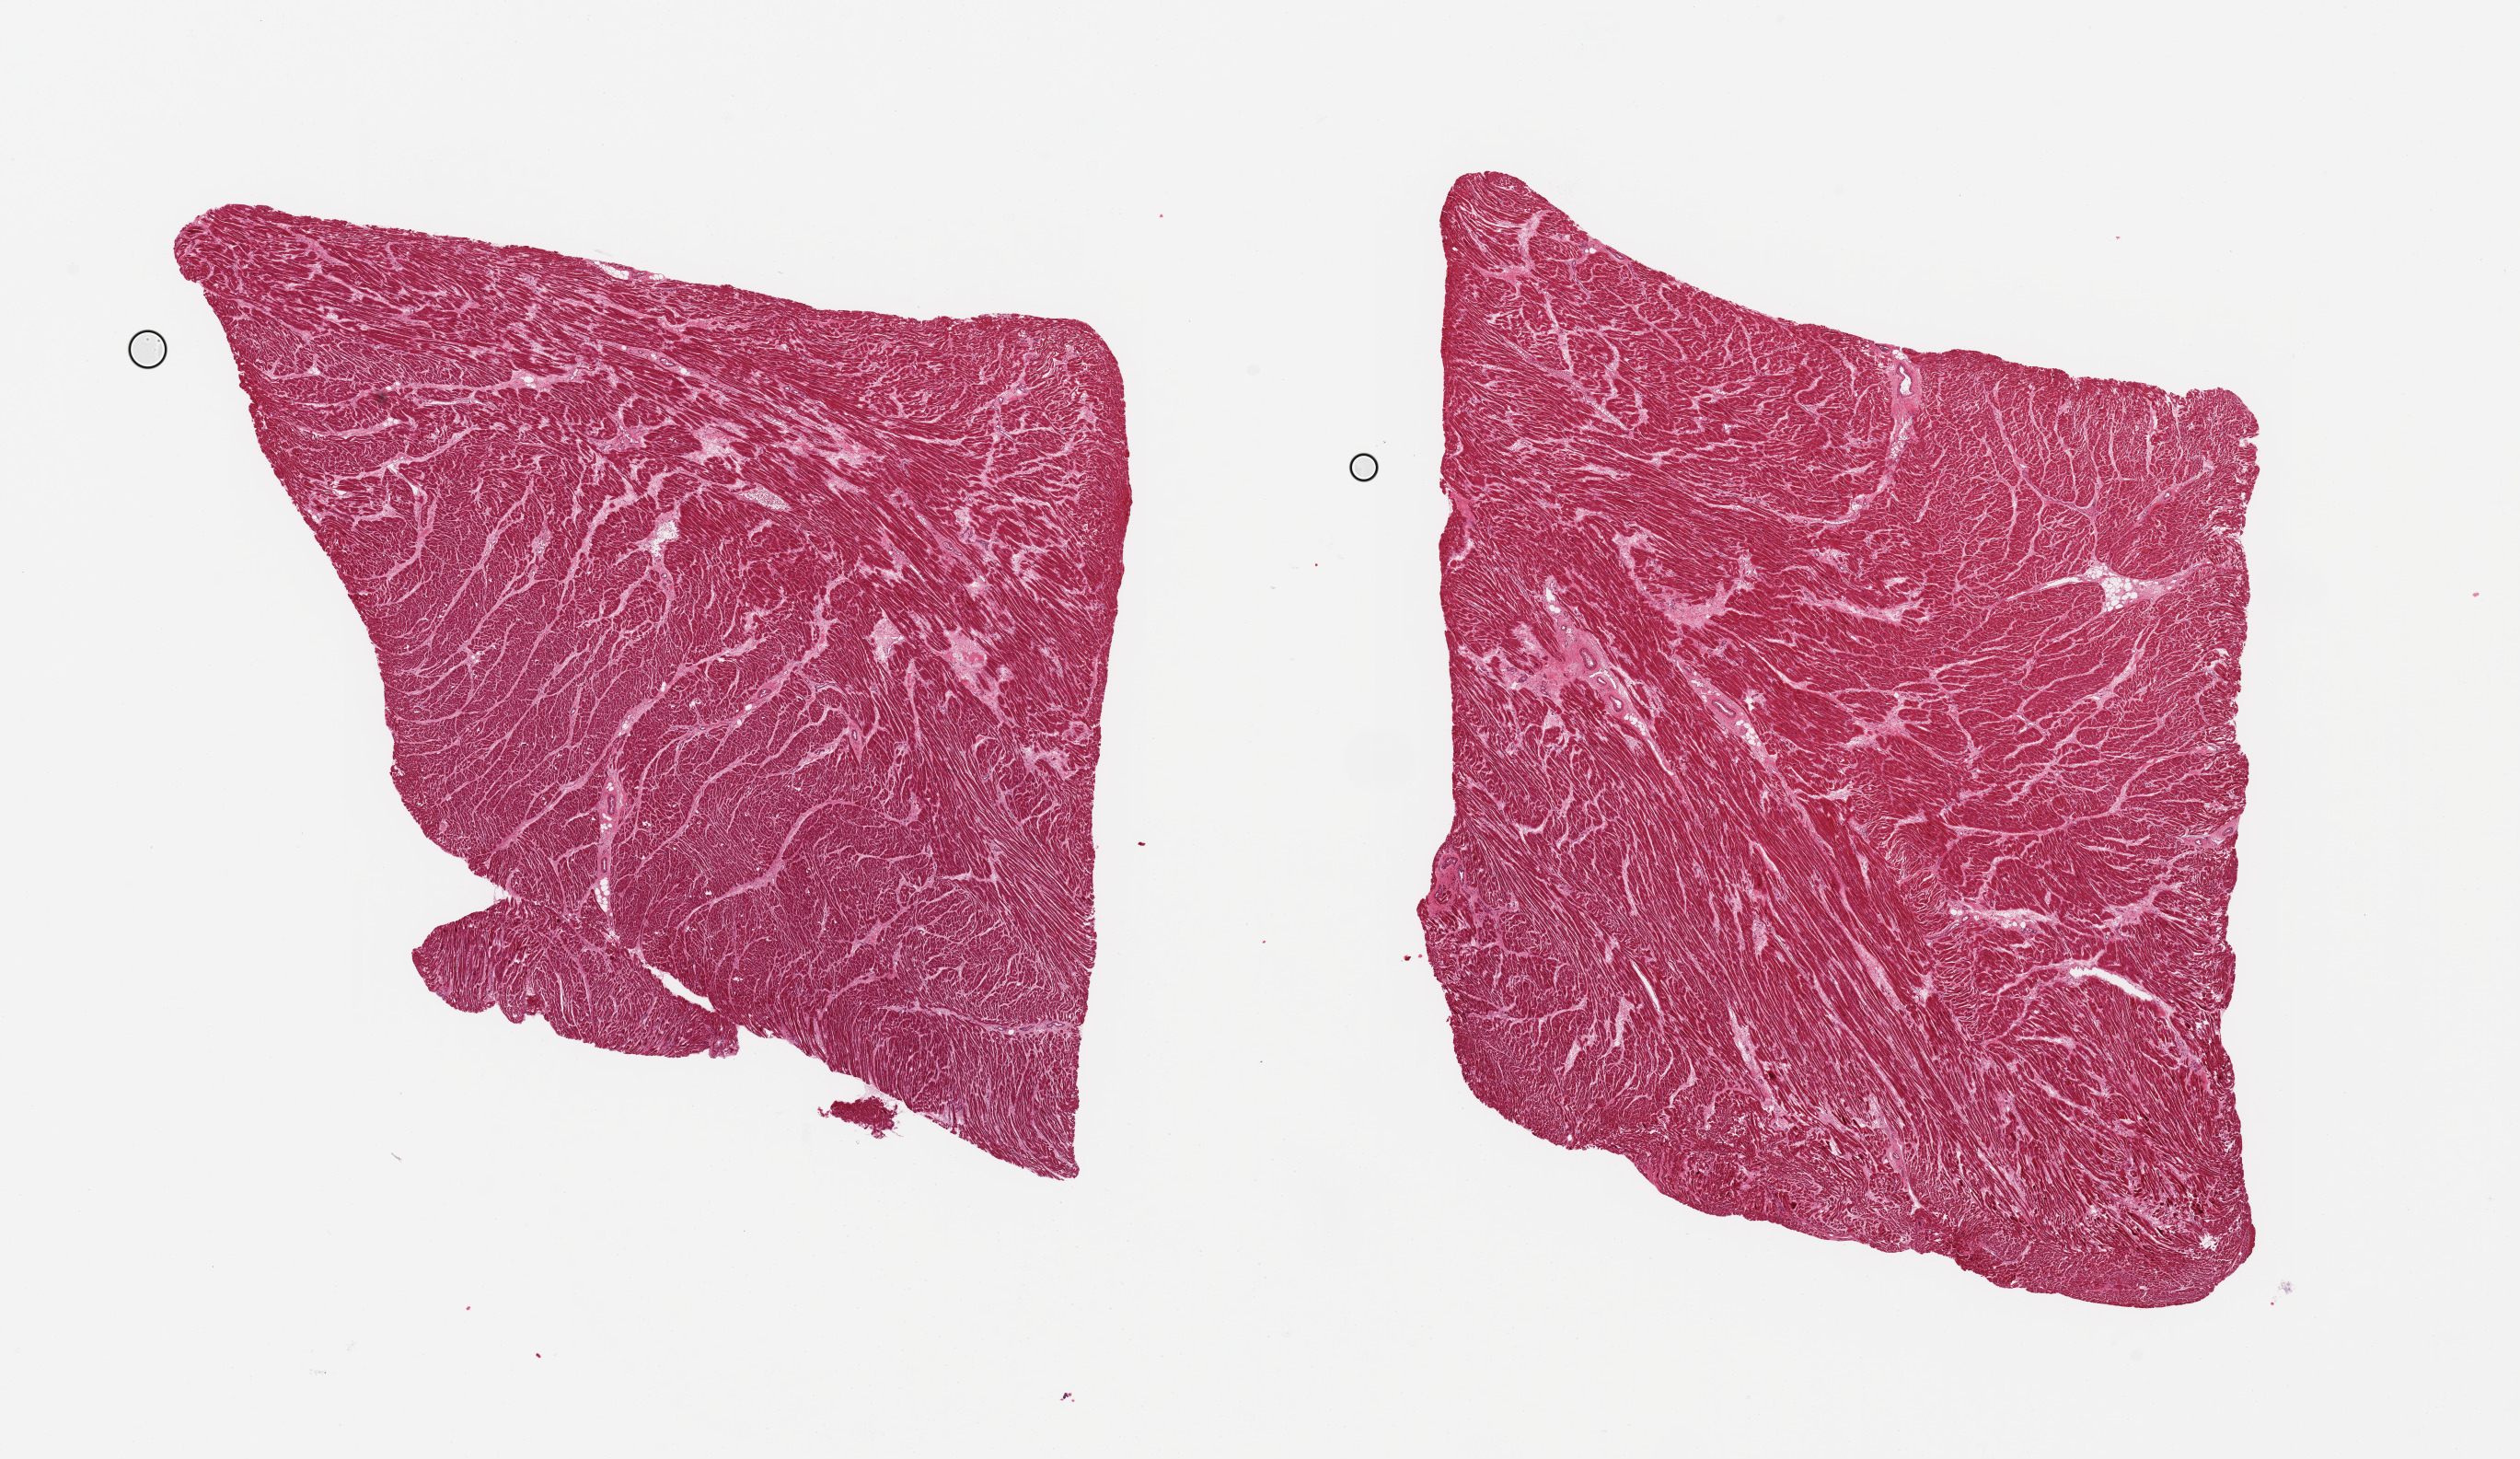
Haematoxylin and eosin whole-slide image, brightfield, shown as a low-resolution overview of the whole scanned area (about 21.7 x 12.5 mm, slide scanned at 20x). PAXgene-fixed paraffin-embedded (PFPE) section. Section of heart (target tissue). Donor tissue sample. Donor: male.
• reviewer comment on this tissue sample: 2 pieces, 8x7 & 8x7mm; no adipose